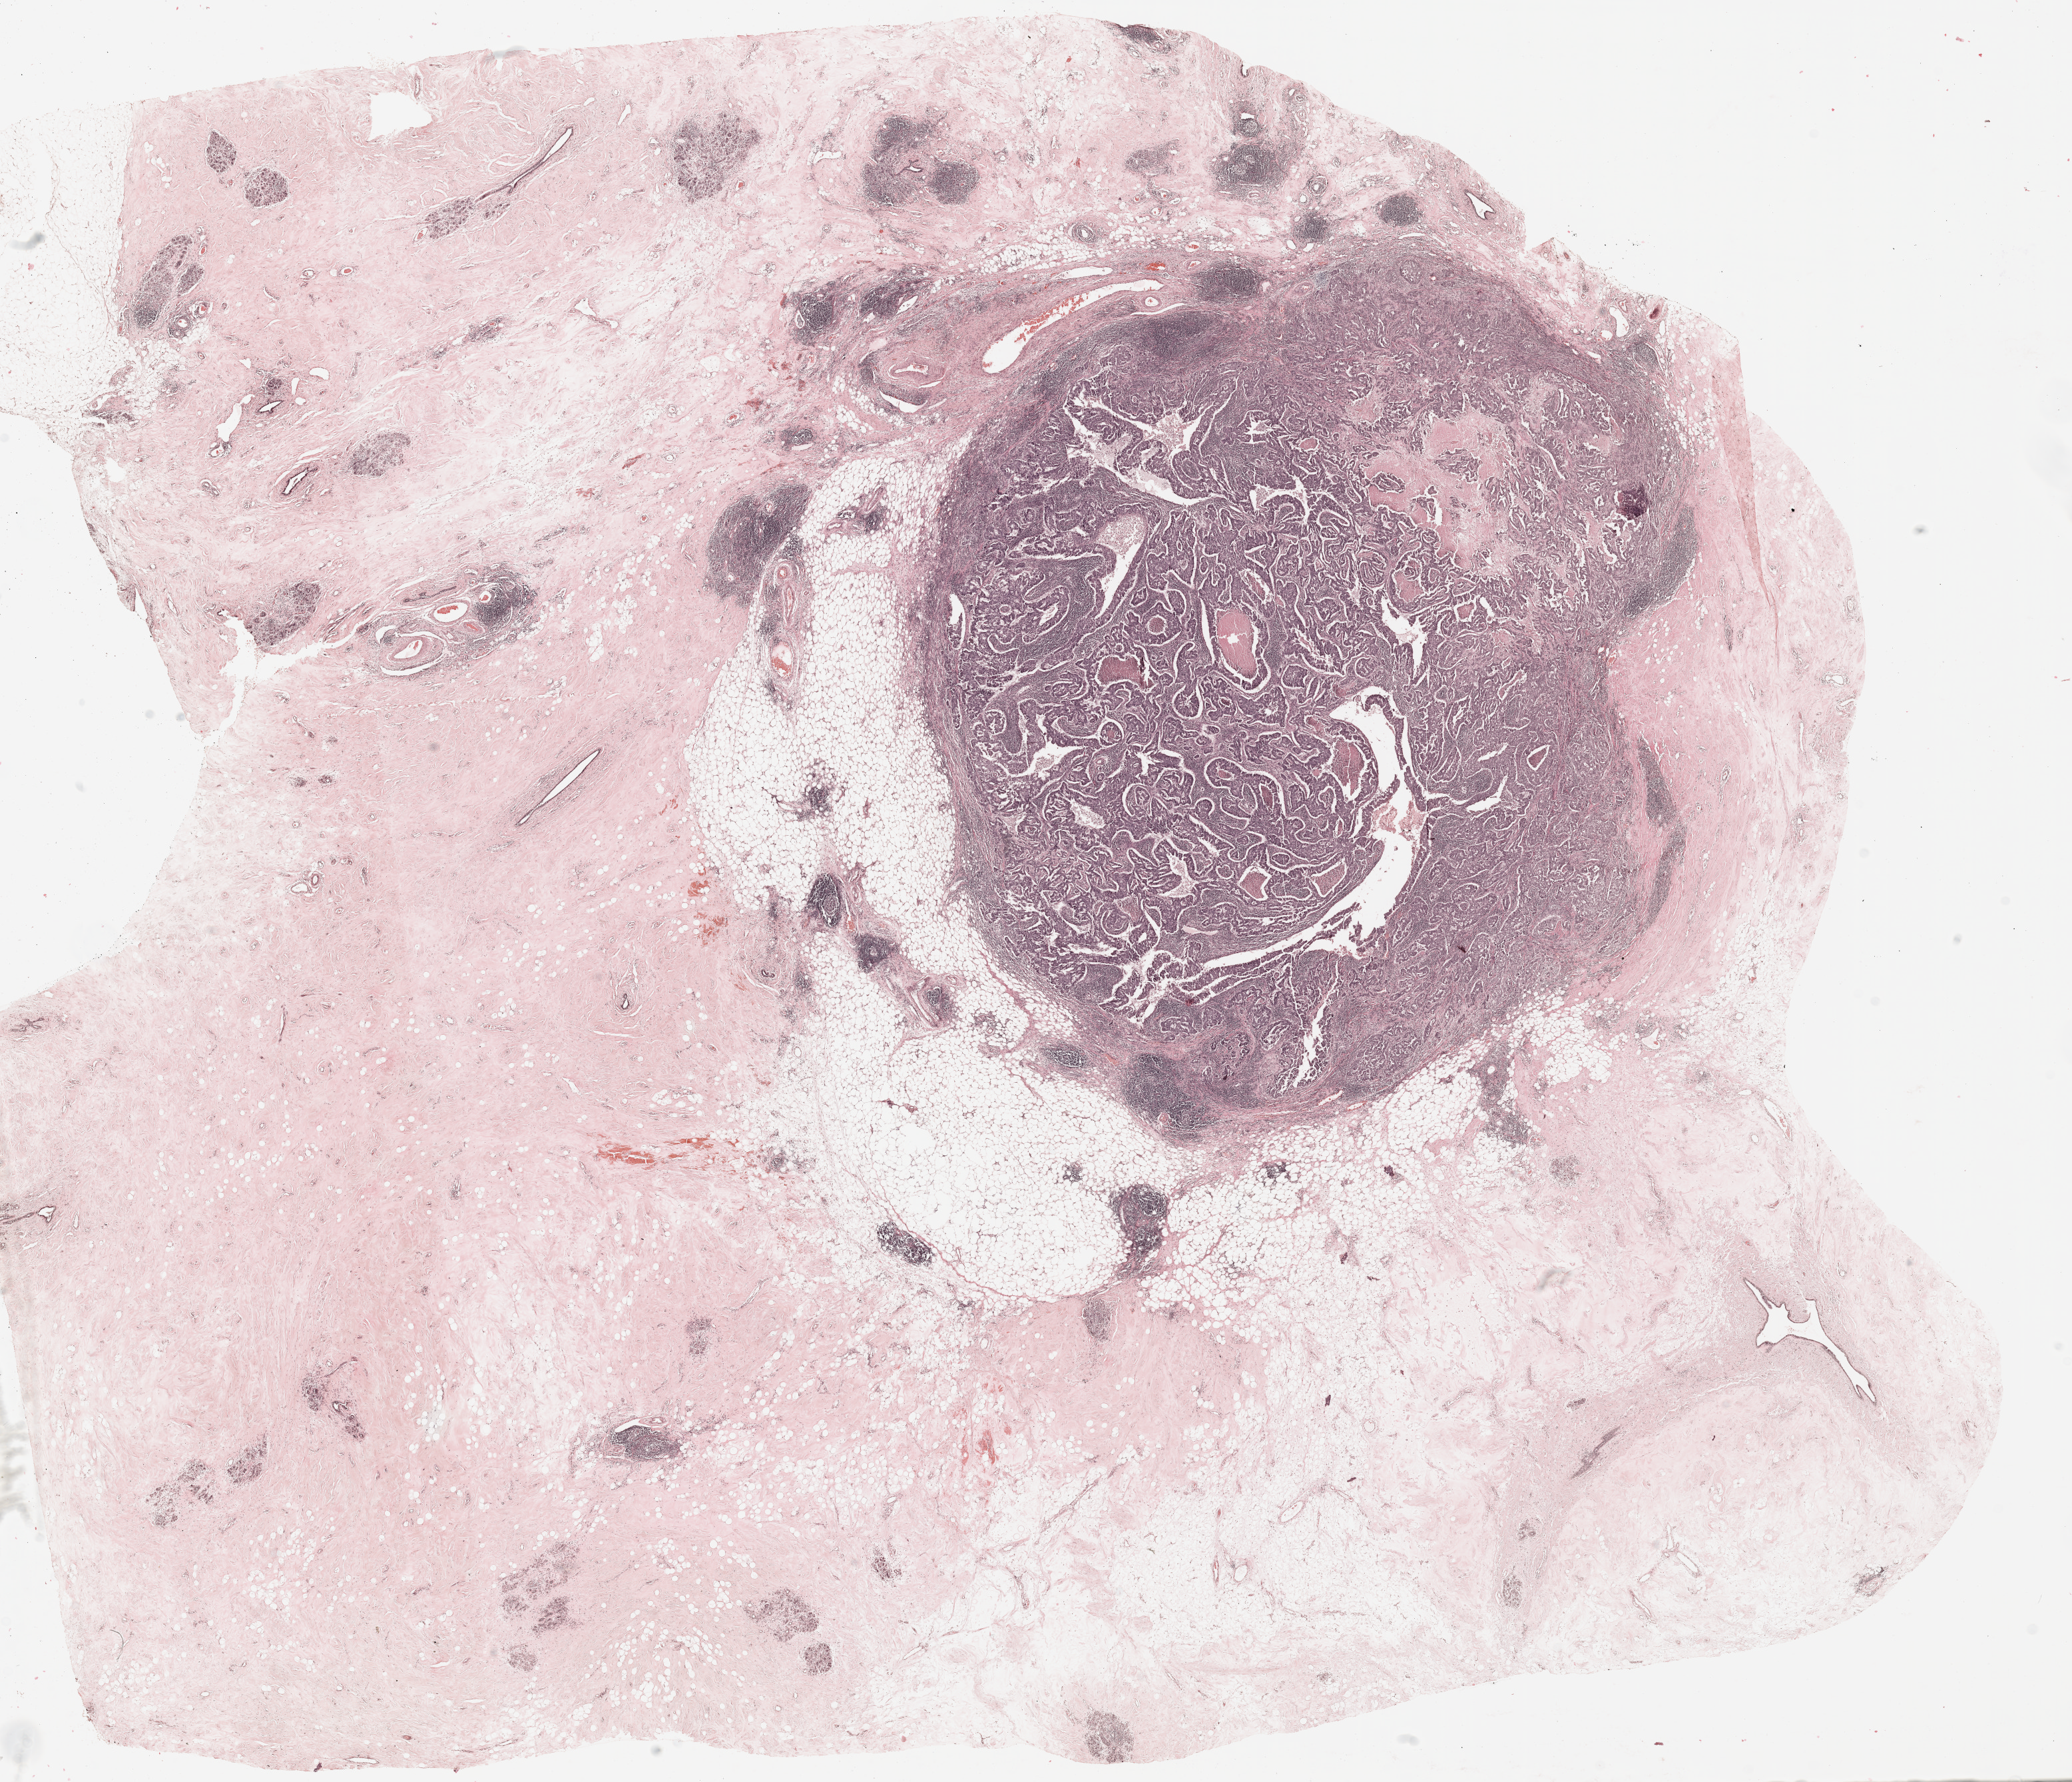
Whole-slide histology image, Hematoxylin and eosin (H&E) stained, a low-resolution overview of the entire scanned area, about 24.9 x 21.4 mm (acquisition: 20x scan), formalin-fixed paraffin-embedded (FFPE) diagnostic section, primary tumour sample from the breast. Patient: female, age at initial diagnosis 29 years.
Histologic diagnosis: Infiltrating duct carcinoma, NOS.